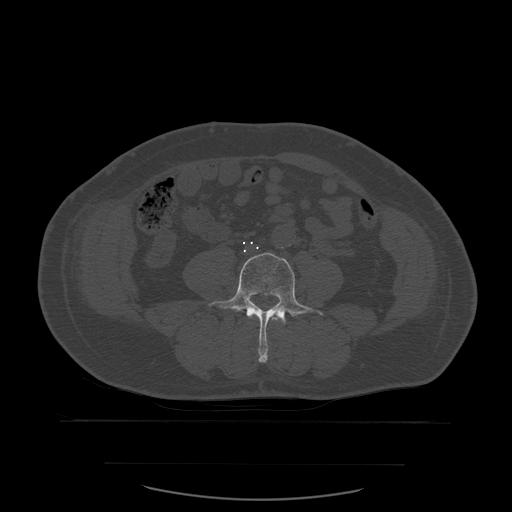
CT including the spine, one axial slice; slice 167 of 590 in the series (ordered by position); bone window (W 1800 / L 400 HU); 1.25 mm slice thickness; 512 × 512 image matrix. Patient age 71 years. From the clinical record (not read from this slice): primary cancer: lung.
Outlined on this slice (semi-automatic segmentation, software-assisted and operator-edited):
- L3 vertebra: box from (x=255, y=313) to (x=284, y=323) px
- L4 vertebra: (x=209, y=253)–(x=323, y=363)